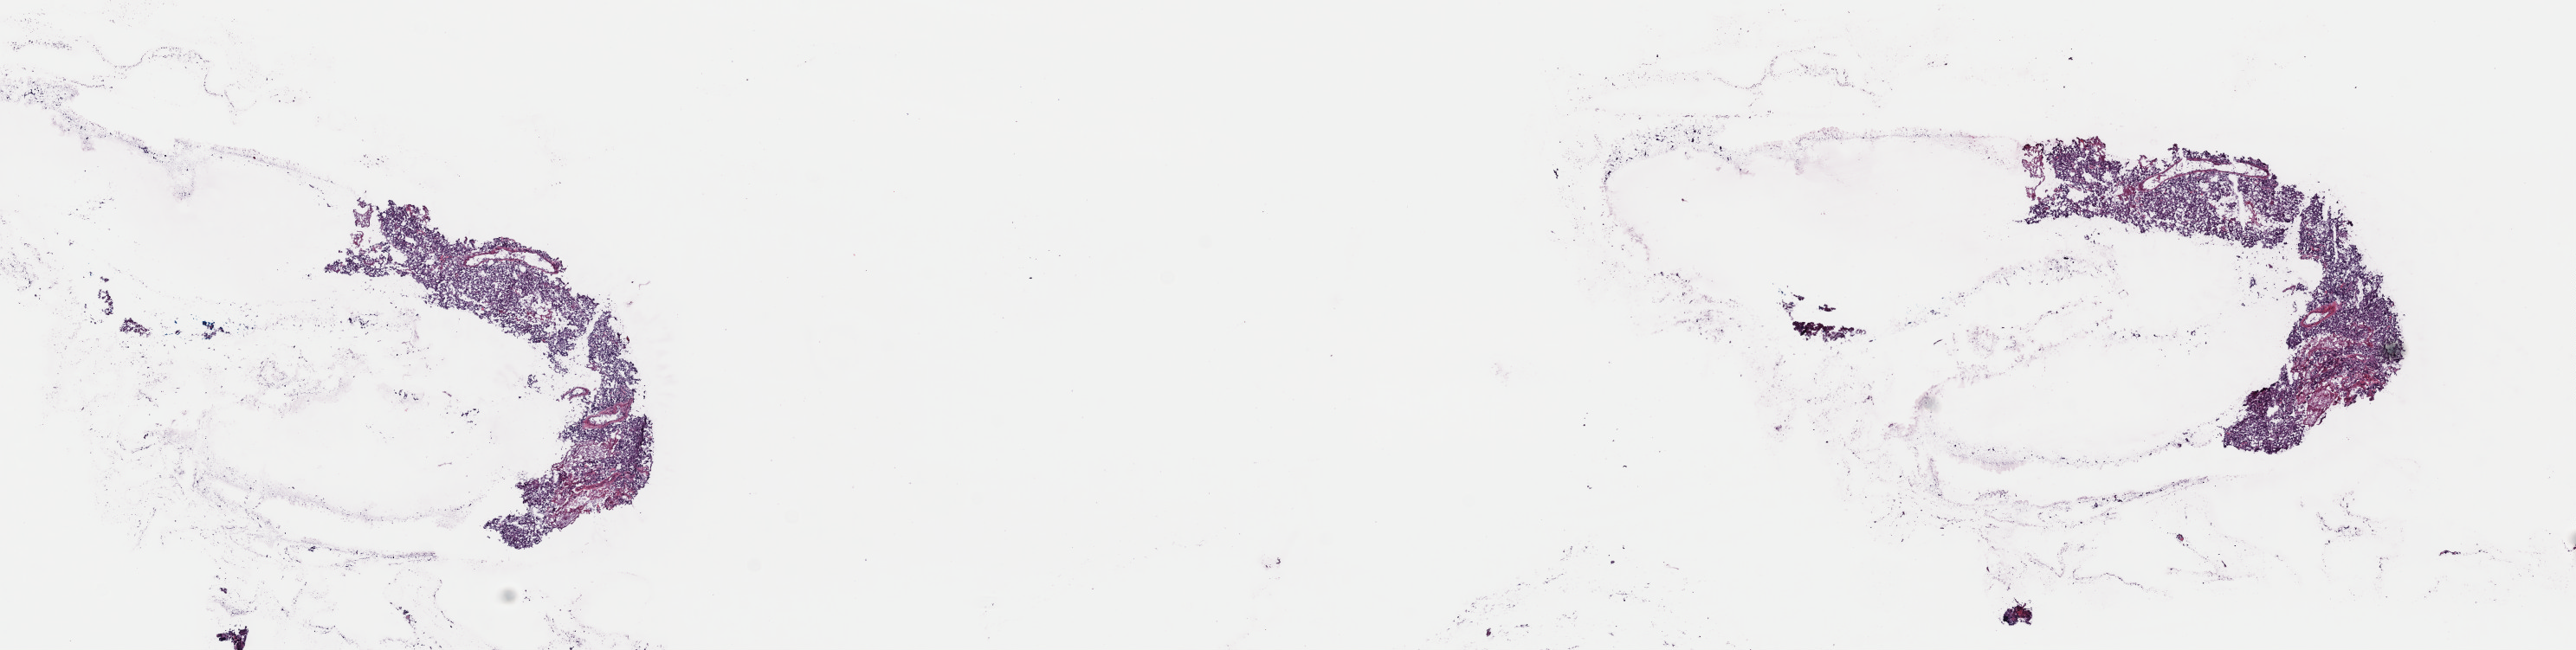
Whole-slide histology image, H&E-stained, shown as a low-resolution overview of the whole scanned area (about 23.5 x 5.9 mm, from a 40x scan), frozen section from the top of the tissue portion, primary tumour sample from the adrenal gland. Patient: female, age at initial diagnosis 64 years. Slide review estimates, as recorded: tumour cells 100%, tumour nuclei 80%.
Pathologic diagnosis: Pheochromocytoma, NOS.